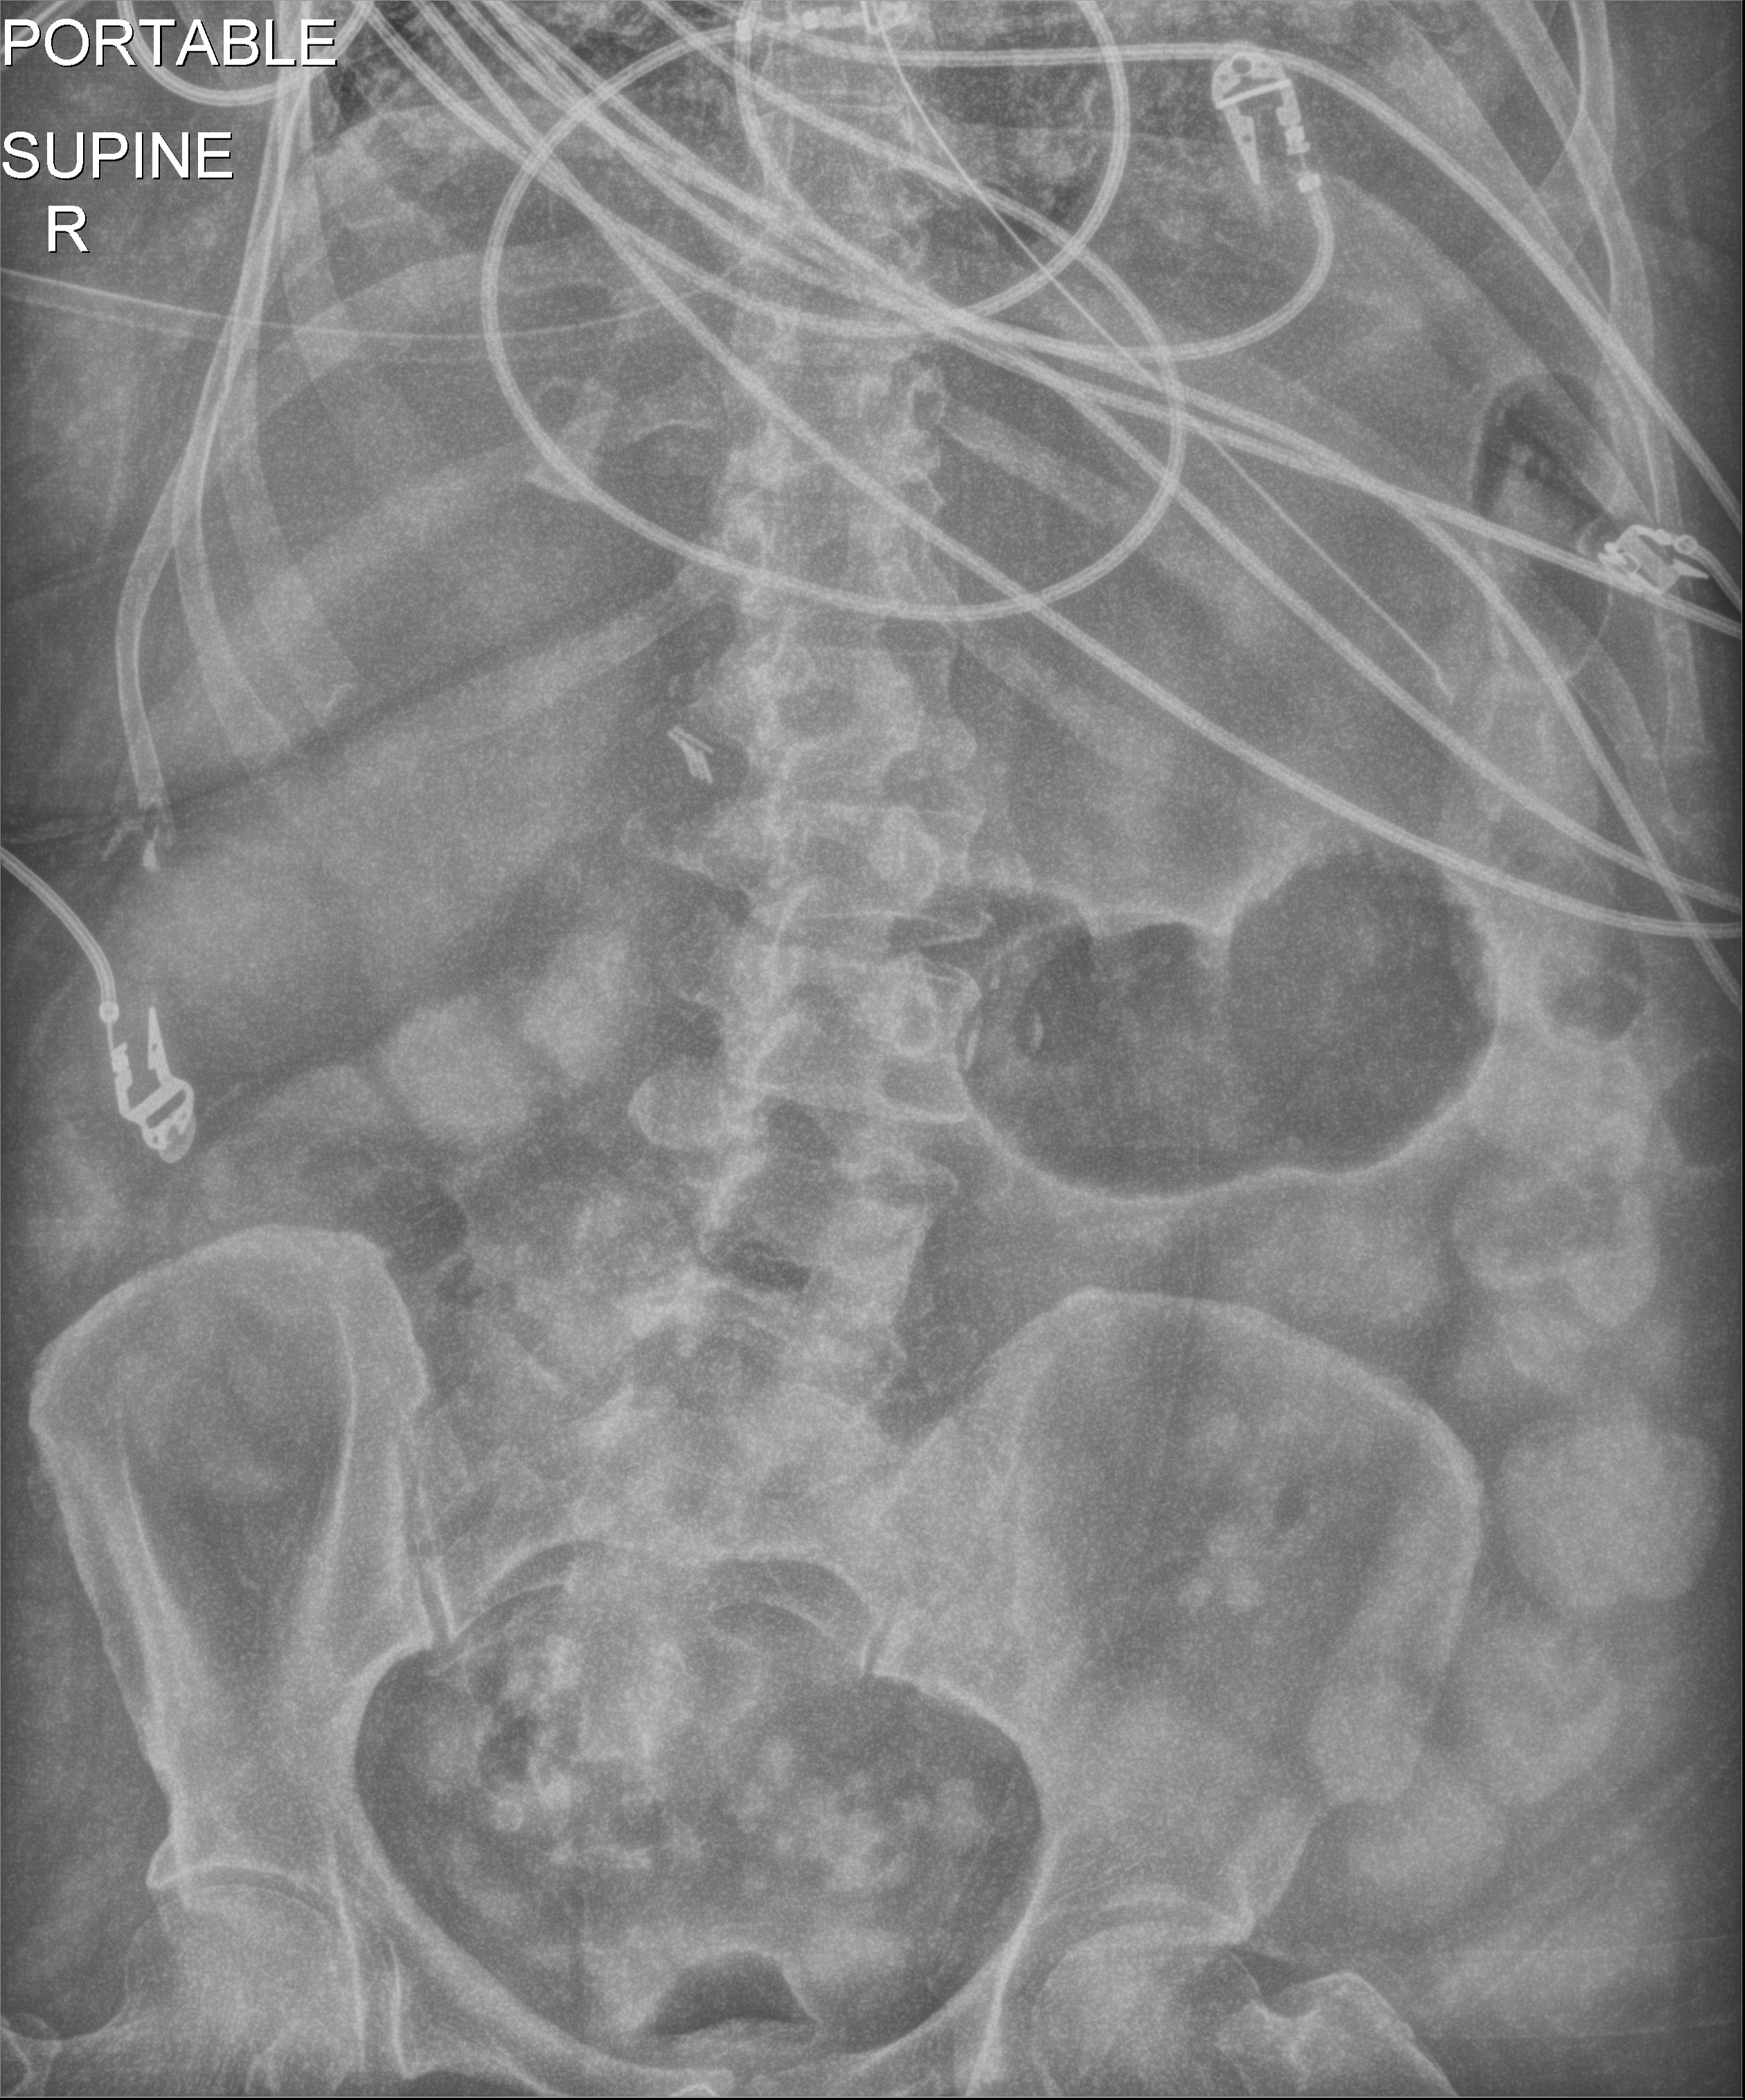
Portable abdomen radiograph; anteroposterior (AP) projection. Female patient hospitalised with COVID-19, age 60–74 years.
Hospital-stay facts (about this admission, not read from this image; timing relative to this image not recorded): length of hospital stay: 45 days.